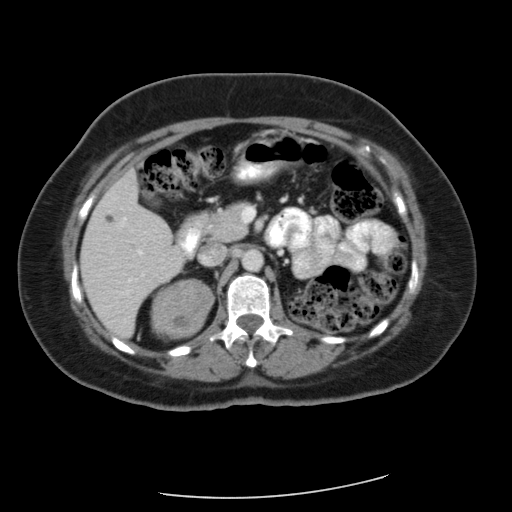
Contrast-enhanced abdominal CT, one axial slice. Position 33 of 56 along the scan axis. 120 kVp. Soft-tissue window (W 400 / L 40 HU). 5 mm slice thickness. 512 × 512 image matrix, field of view 400 × 400 mm. Patient: female, 58 years. From the clinical record (not read from this slice): diagnosis: adrenocortical carcinoma; tumour side: right adrenal.
Outlined on this slice (semi-automatic segmentation, software-assisted and operator-edited):
- mass: bounding box <152,280,212,336> (left, top, right, bottom; pixels)